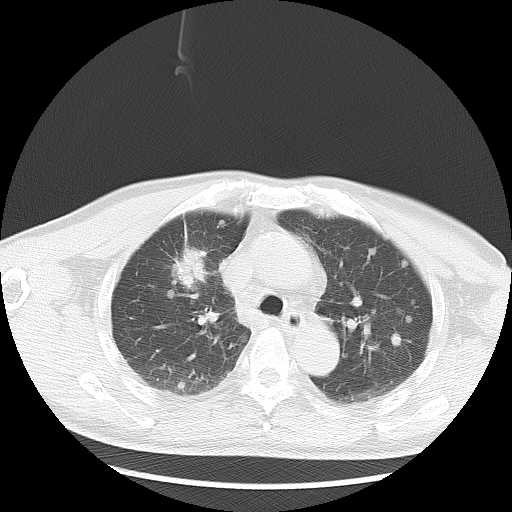
Chest CT, one axial slice; position 20 of 35 along the scan axis; reconstruction kernel LUNG; 120 kVp; lung window (W 1500 / L -600 HU); 5 mm slice thickness; 512 × 512 image matrix. Patient: male, 57 years. Case-level facts recorded for this patient, not image findings: clinical TNM (as recorded): T2 N3 M1a.
Structures marked on this image (rectangle marked by the reading radiologist):
- lung tumour (recorded histology: adenocarcinoma): bounding box [x1, y1, x2, y2] px = [175, 243, 208, 292]